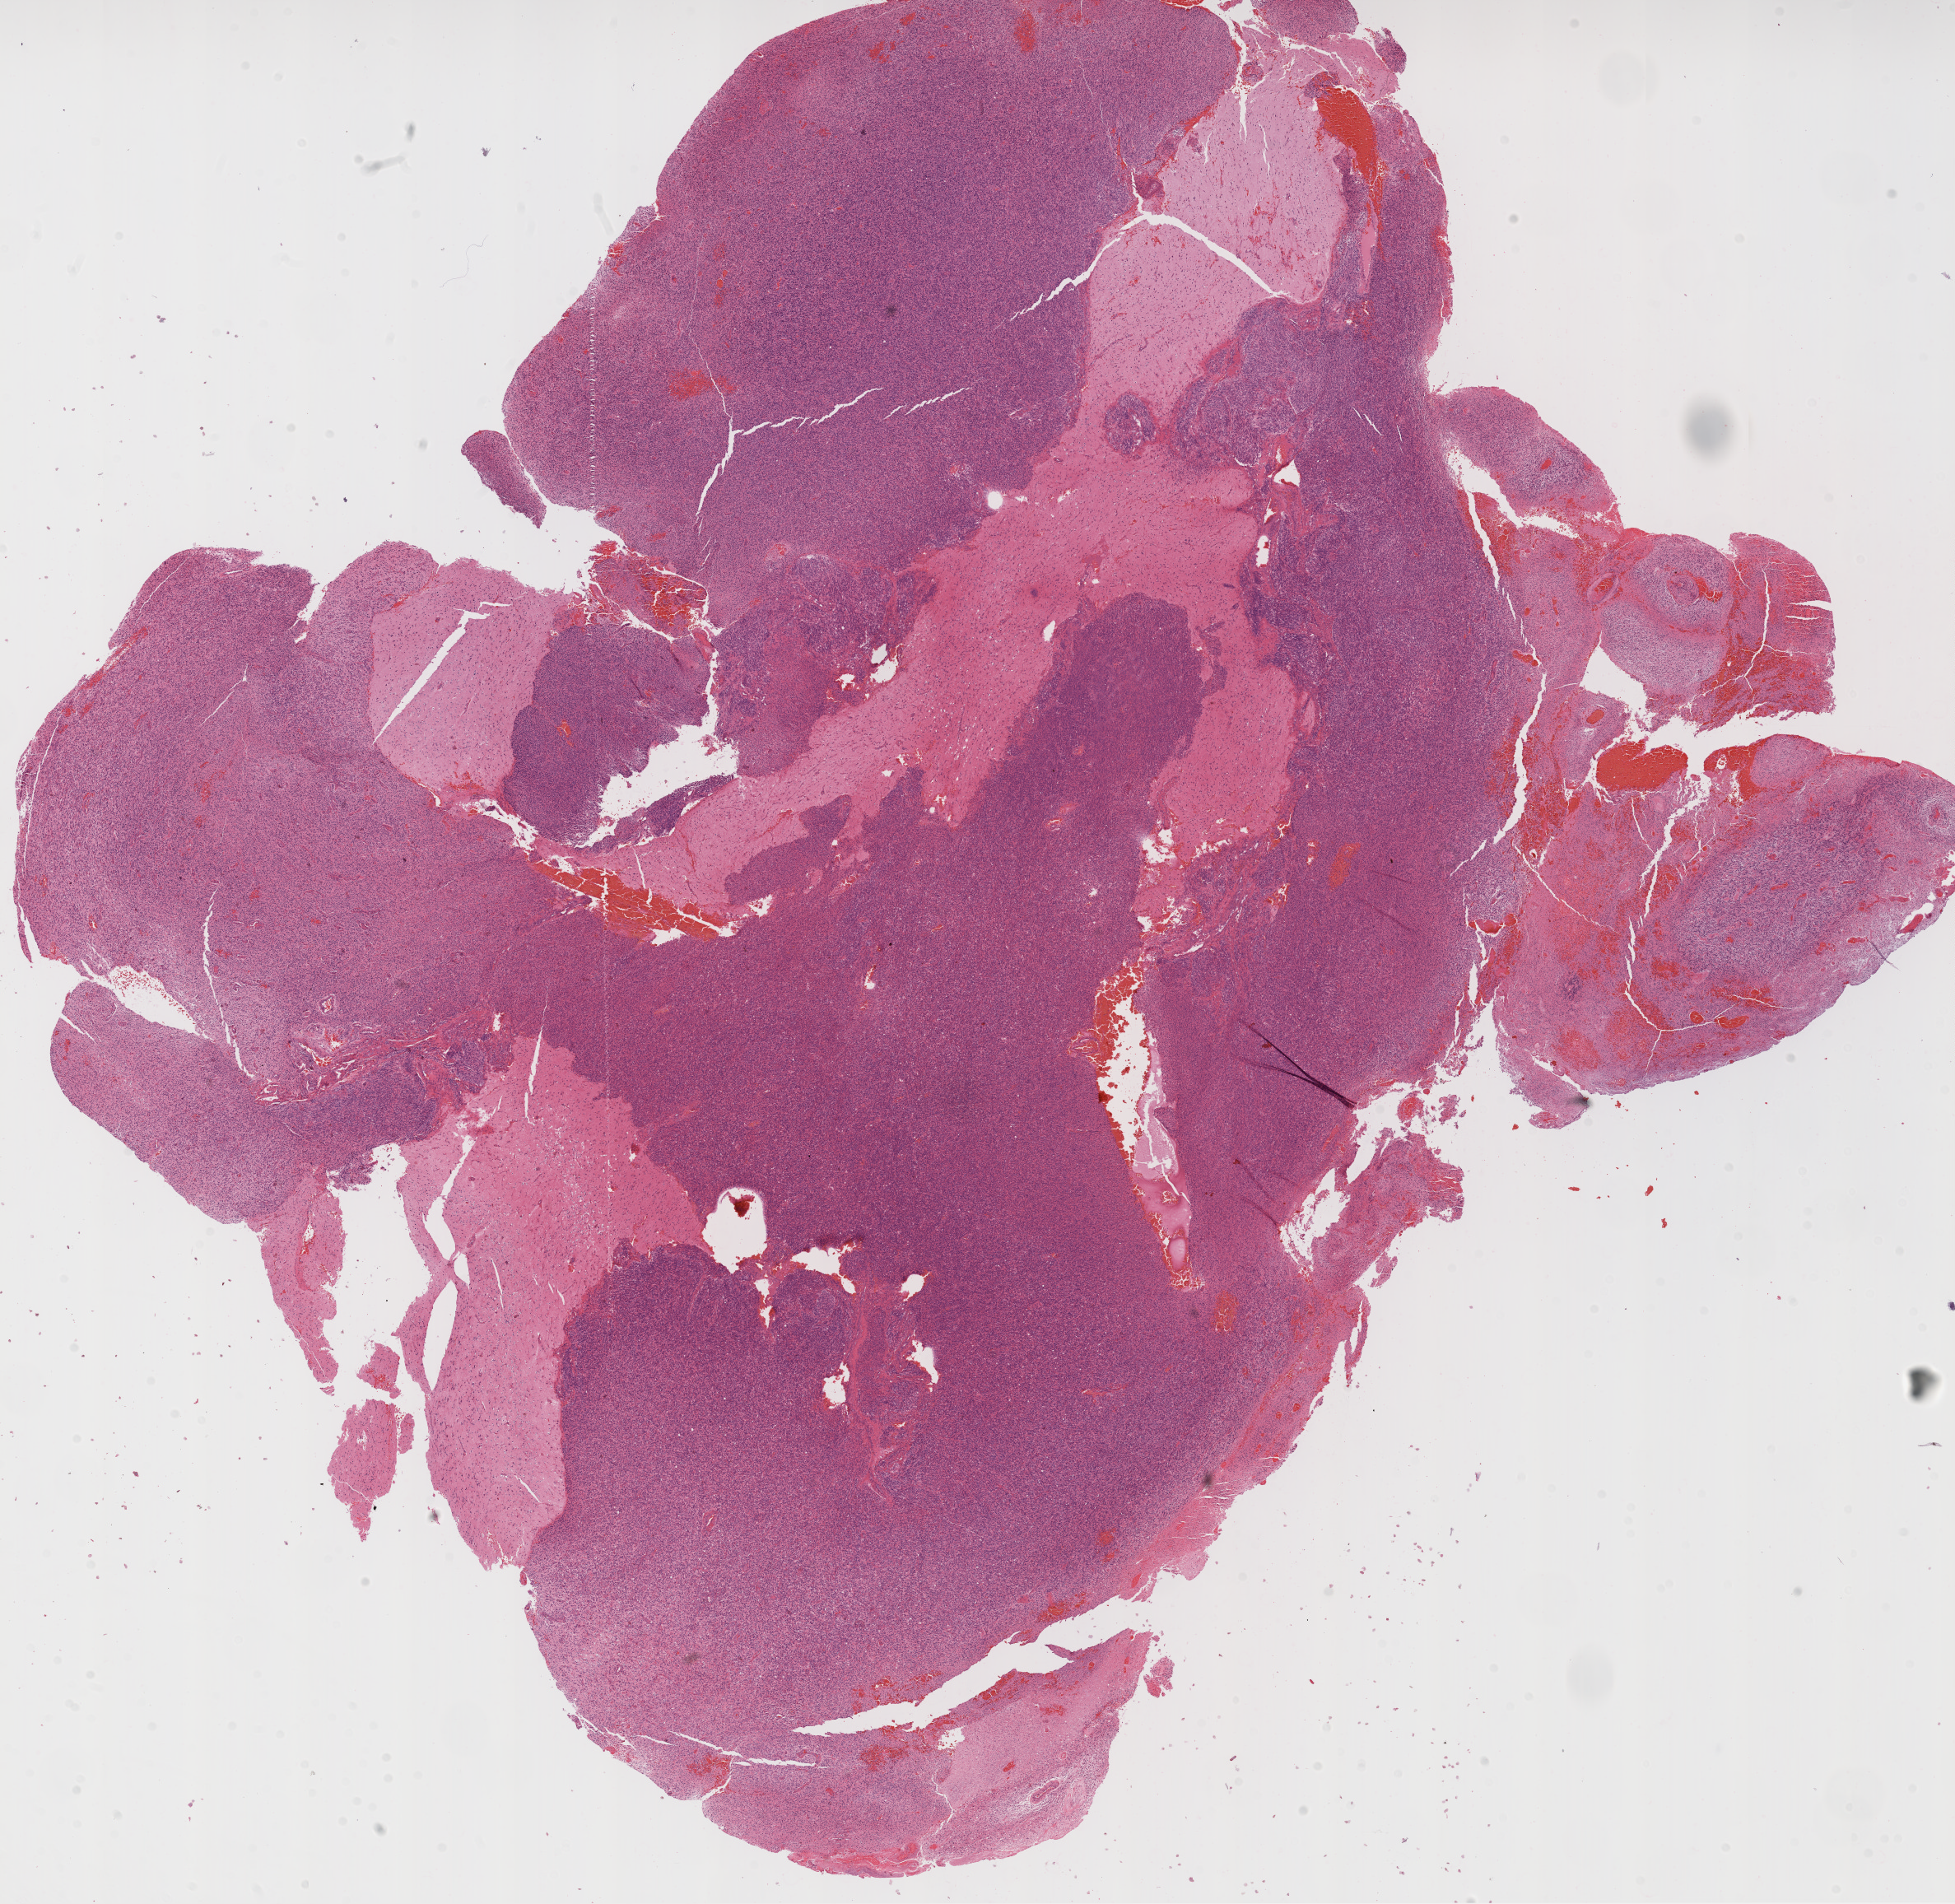
H&E-stained whole-slide image, whole scanned area (about 19.1 x 18.6 mm, slide scanned at 20x) shown as a low-resolution overview. FFPE section. Primary tumour sample from the brain. Male patient; age at initial diagnosis 76 years.
Histologic diagnosis: Glioblastoma.